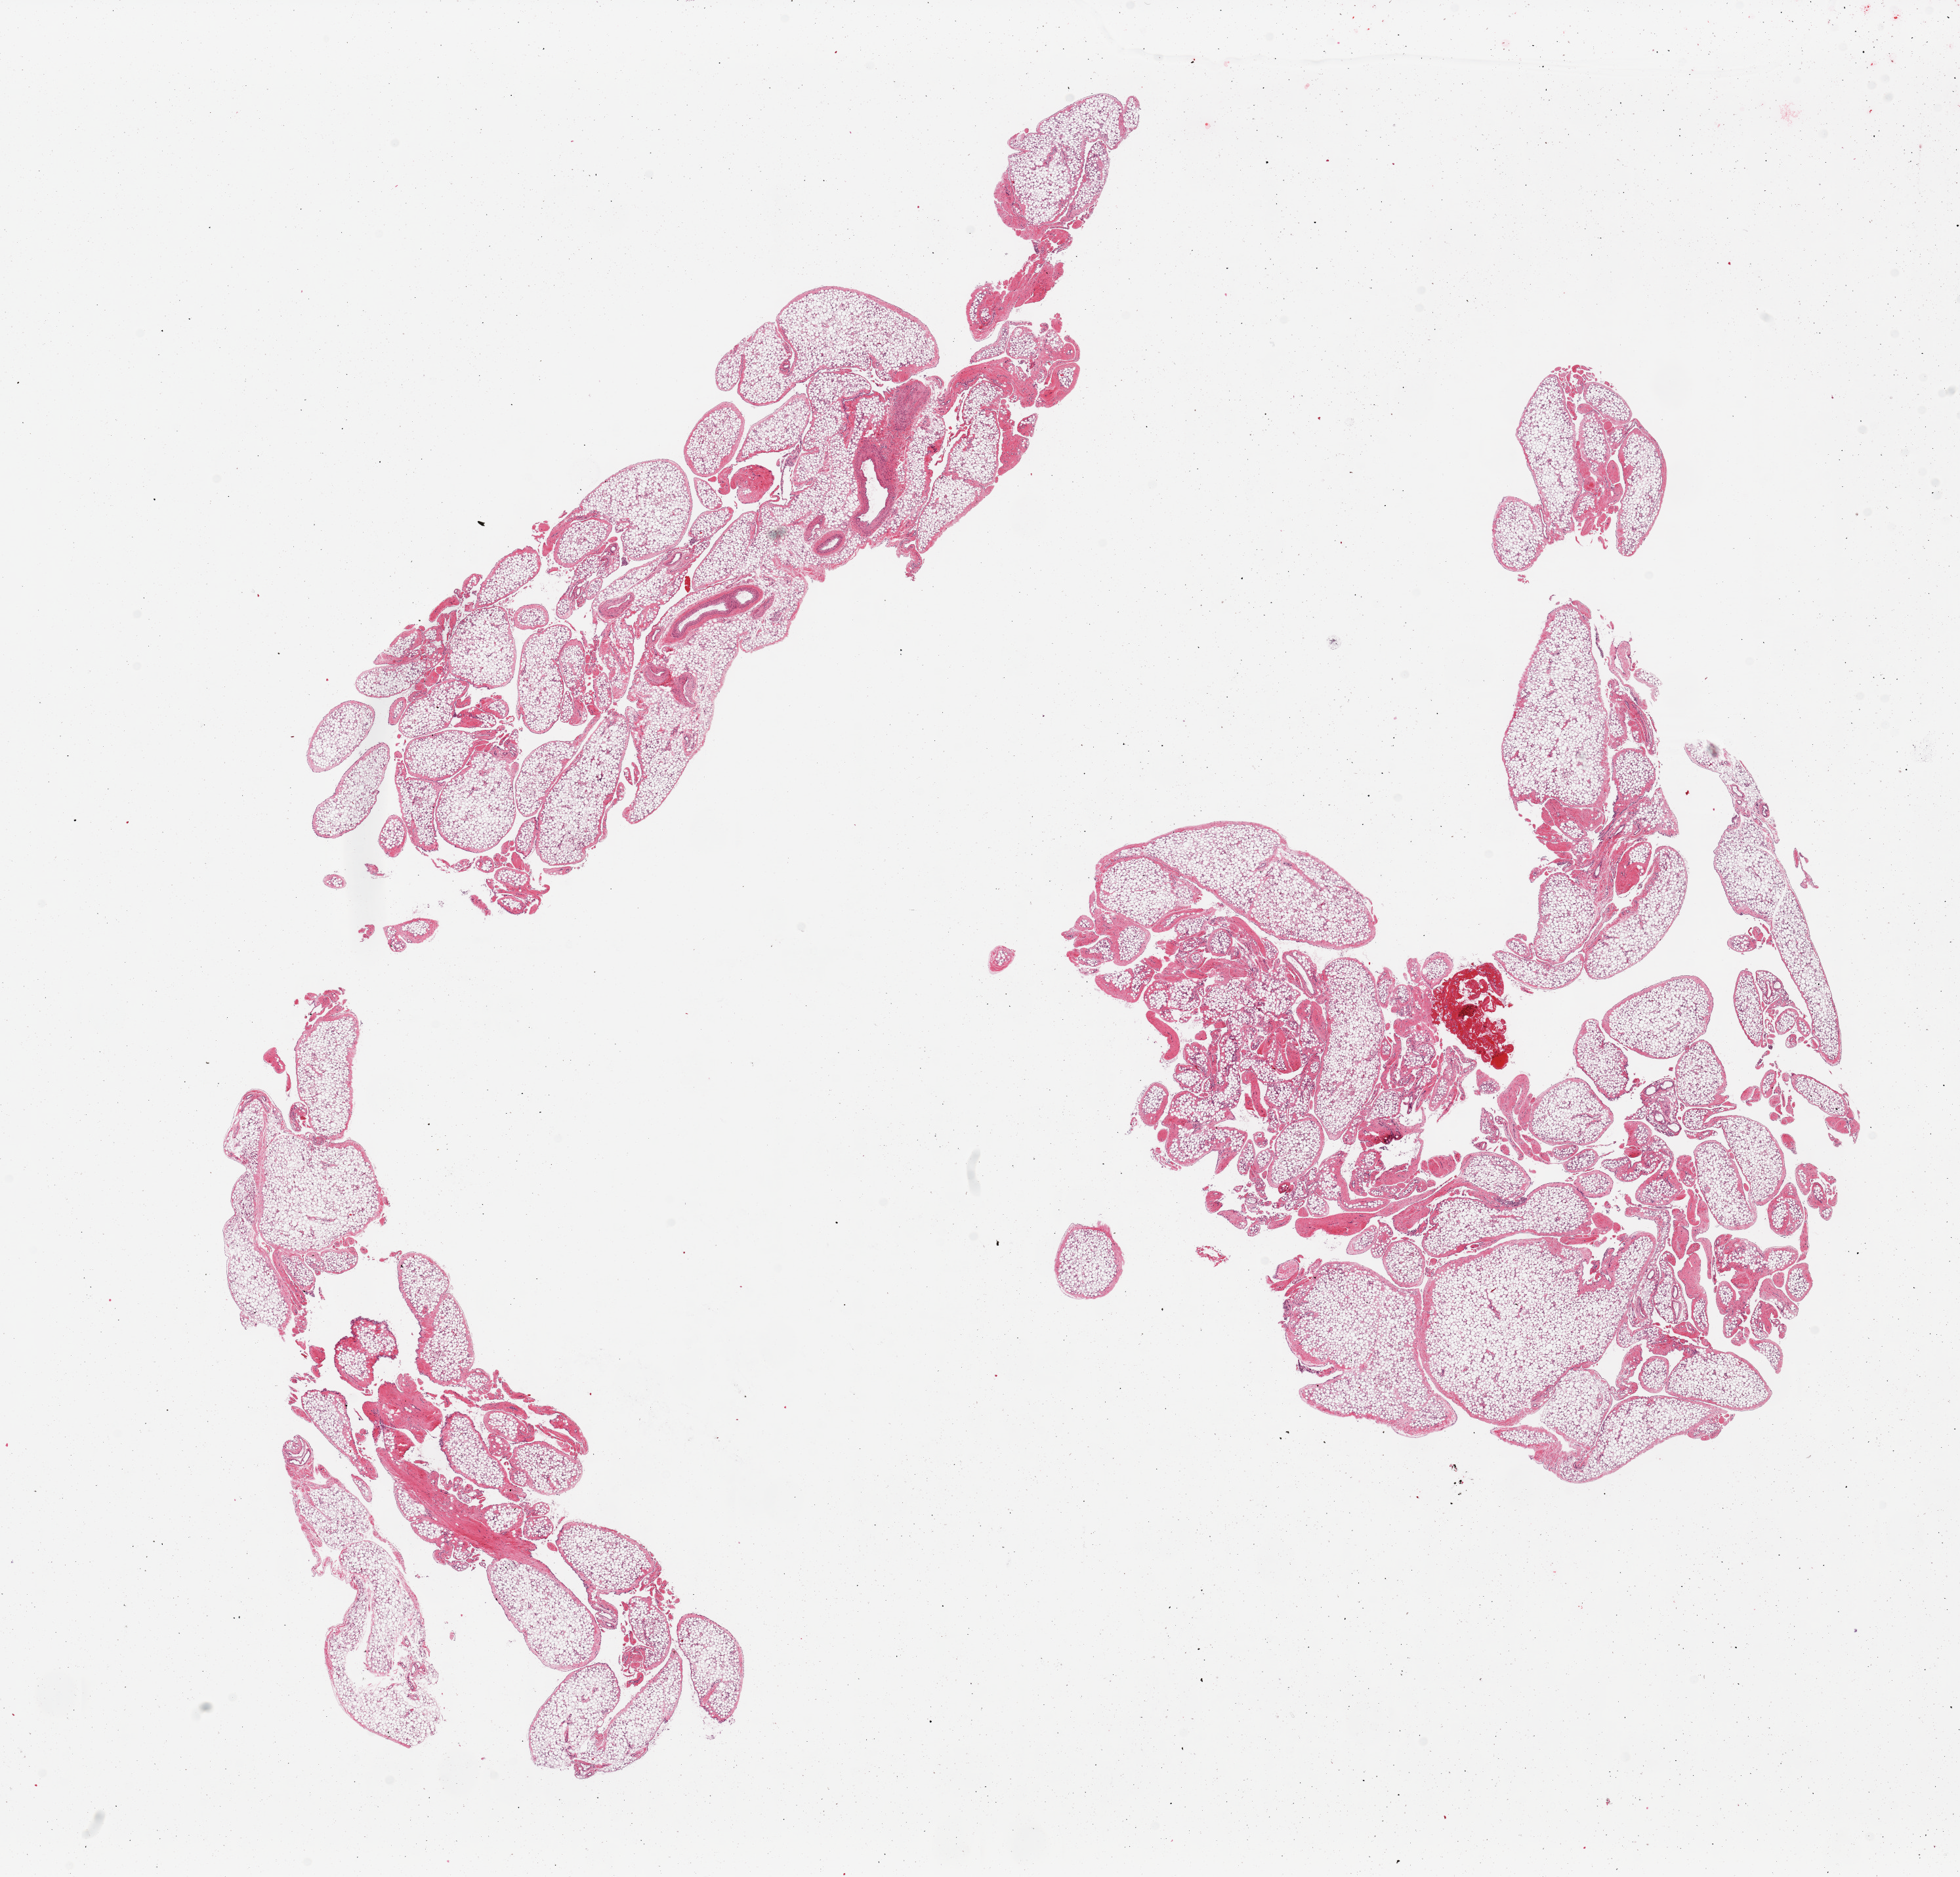
Digitized hematoxylin and eosin (H&E)-stained section — shown as a low-resolution overview of the whole scanned area (about 23.6 x 22.6 mm, acquisition: 20x scan). PAXgene-fixed paraffin-embedded (PFPE) section. Sampled site (target tissue): omentum. Donor tissue sample. Male donor.
* review note (as recorded): 2 pieces; more submesothelial fibrosis than usual. No vasculitis